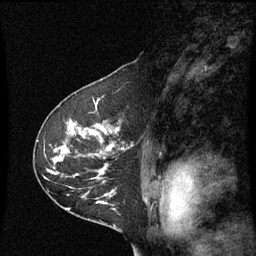
Breast MRI (dynamic contrast-enhanced), one sagittal slice. Position 41 of 60 along the scan axis. Dynamic contrast-enhanced series, image 2 of 3 at this slice position (ordered by acquisition). 1.5 T. TE 4.2 ms, TR 8.9 ms. 2 mm slice thickness. 256 × 256 image matrix, field of view 200 × 200 mm. Patient: female, 53 years. Case-level facts recorded for this patient, not image findings: setting: breast cancer imaged before/during neoadjuvant chemotherapy; receptor status: HR-positive, HER2-negative.
Outlined on this slice (semi-automatic segmentation, software-assisted and operator-edited):
- analysis volume of interest (the breast-tissue region the enhancement analysis was run in; not a lesion): box from (x=34, y=100) to (x=145, y=221) px
- tumour enhancement mask (voxels above the 70 % enhancement threshold inside the analysis volume of interest): (x=54, y=126)–(x=119, y=189)